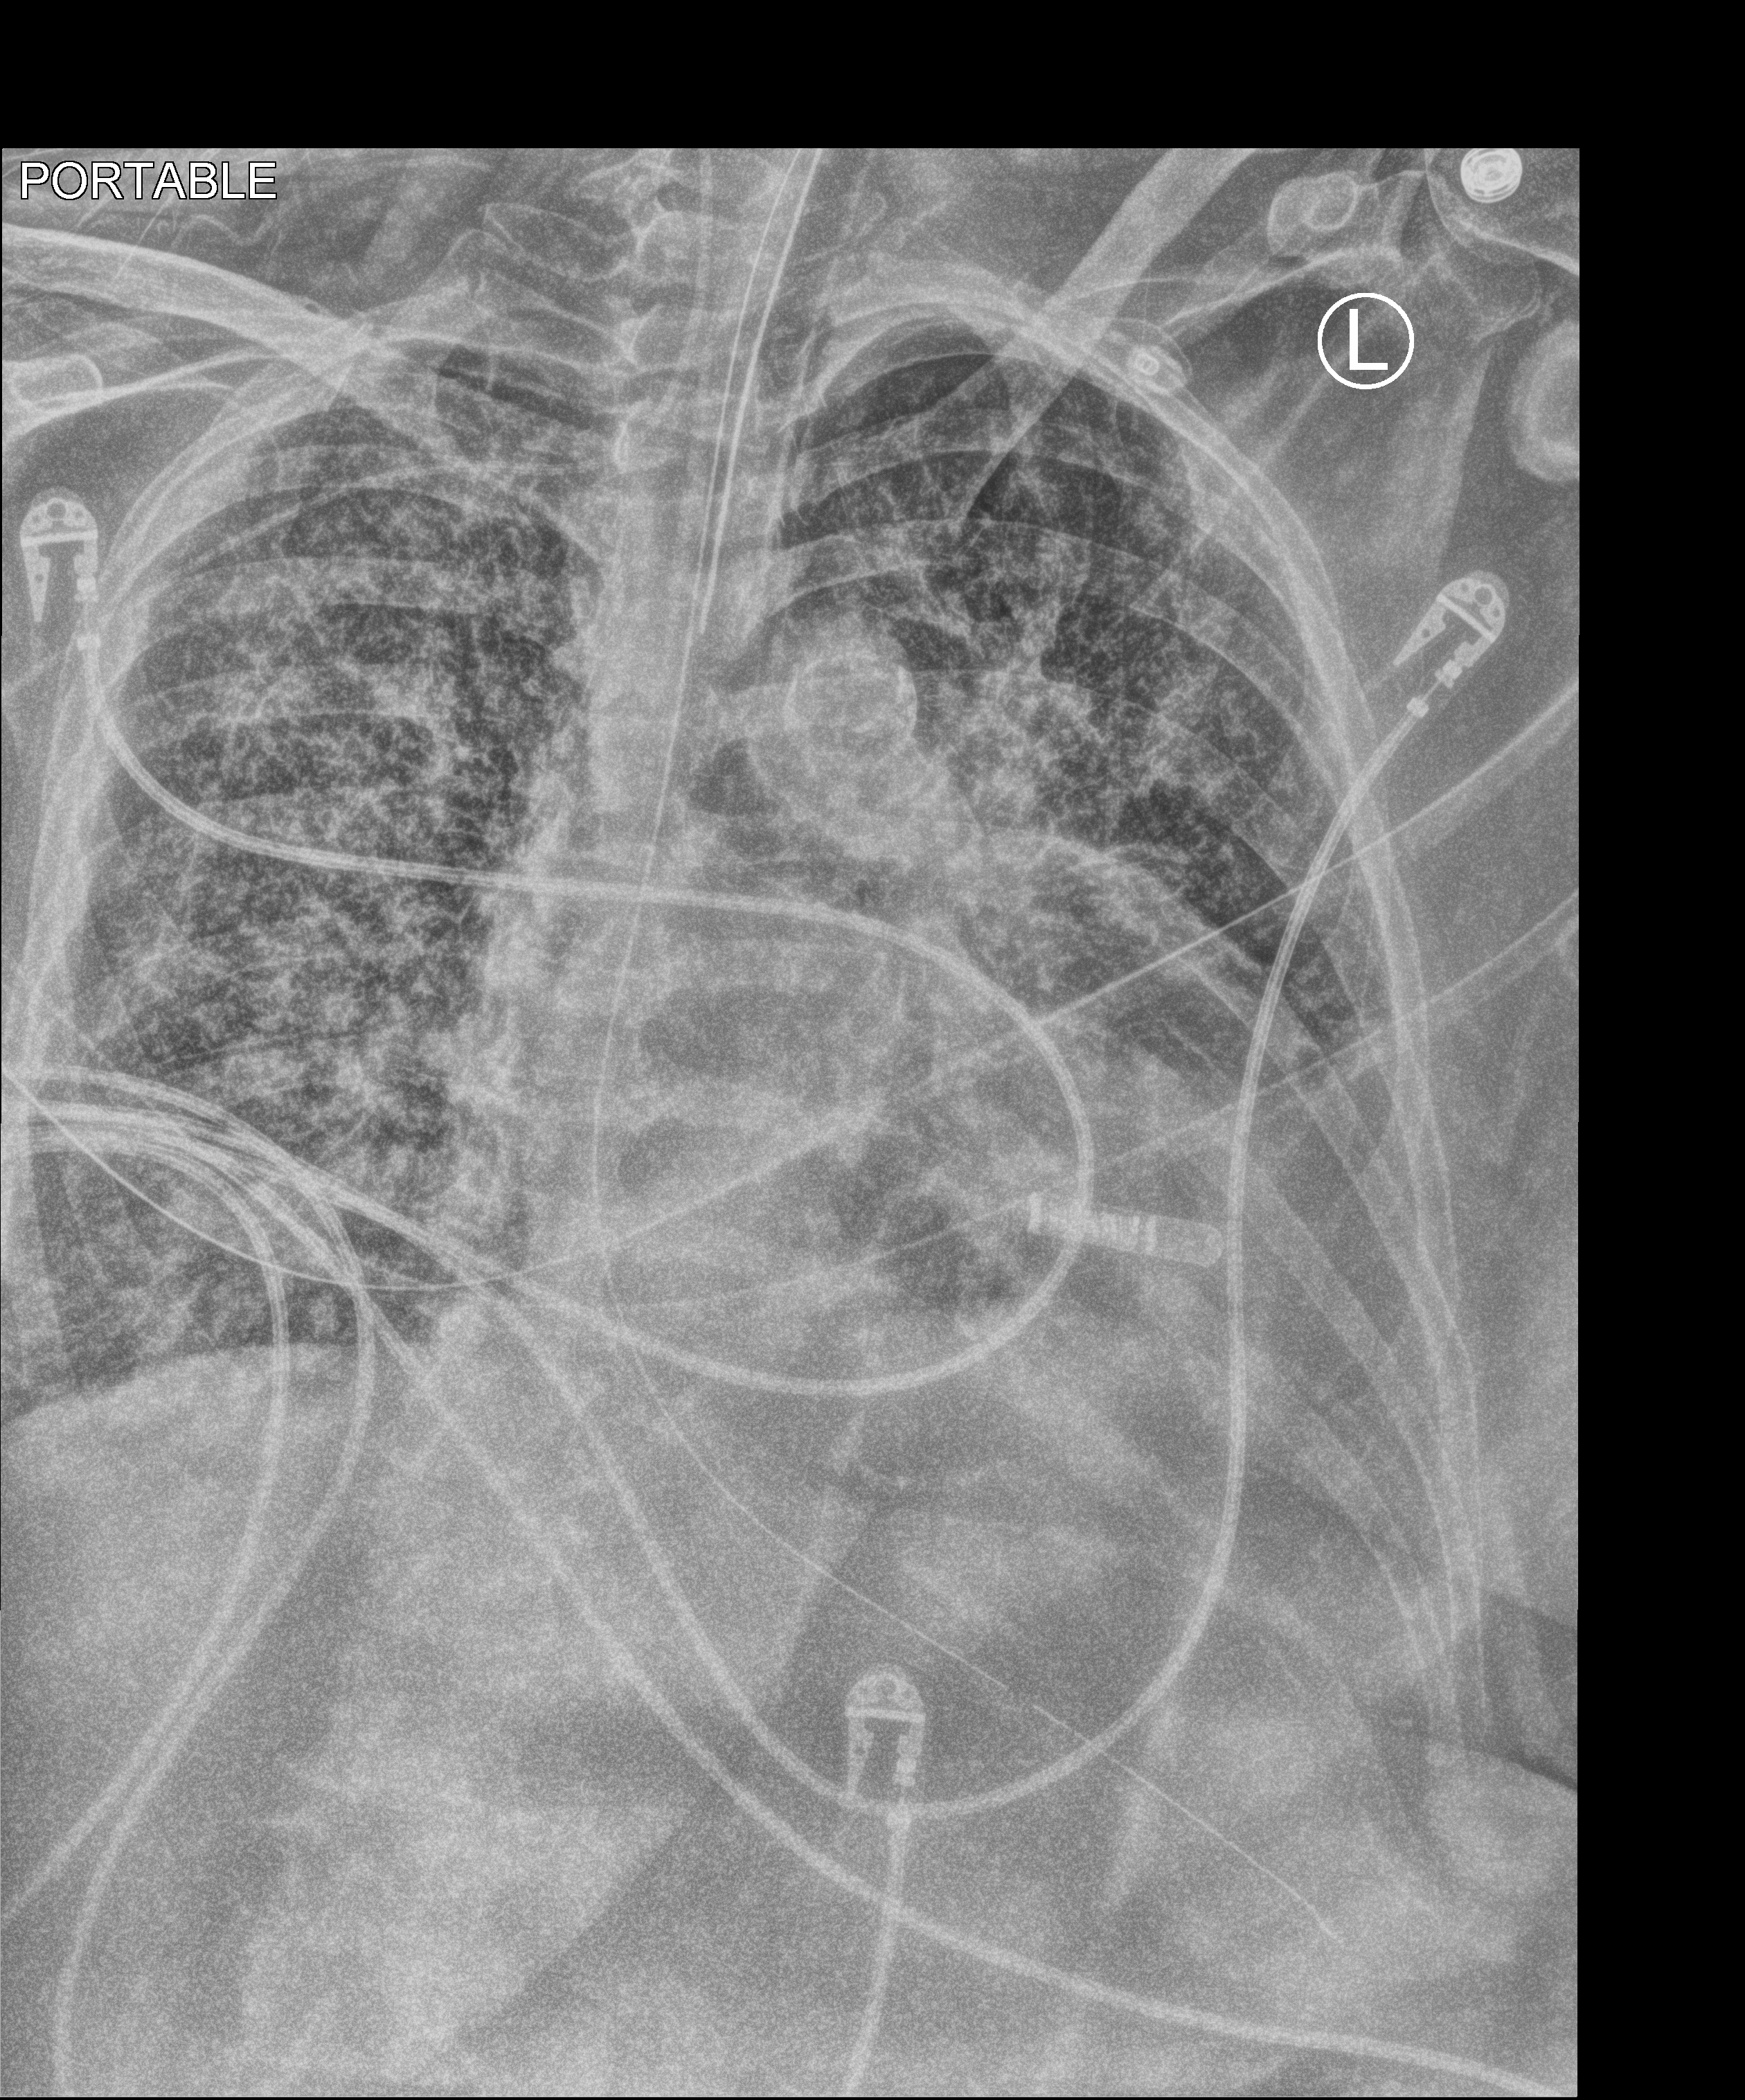
Chest X-ray (portable), anteroposterior (AP) projection. Female patient hospitalised with COVID-19, age 60–74 years.
From the hospital-stay record, not from the radiograph (when in the stay this image was taken is not recorded): COPD (admission record): no; length of hospital stay: 28 days; admitted to intensive care during this hospital stay: yes.